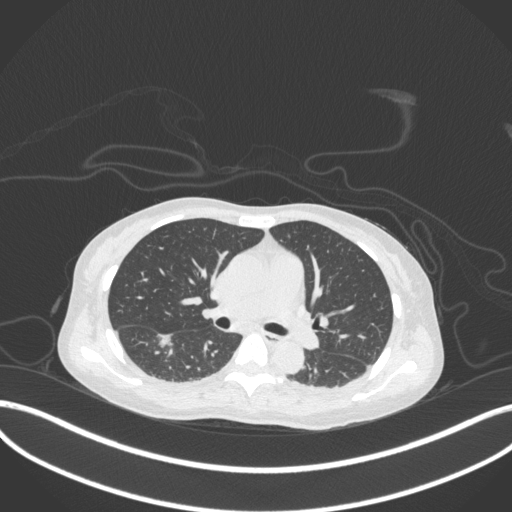
Chest CT, one axial slice; slice 182 of 260 in the series (ordered by position); reconstruction kernel B31f; 120 kVp; lung window (W 1500 / L -600 HU); 1 mm slice thickness; 512 × 512 image matrix, field of view 400 × 400 mm. Patient: female, 44 years. From the clinical record (not read from this slice): clinical TNM (as recorded): T1c N0 M0.
Annotated regions visible in this slice (rectangle marked by the reading radiologist):
- lung tumour (recorded histology: adenocarcinoma): box from (x=156, y=332) to (x=176, y=350) px